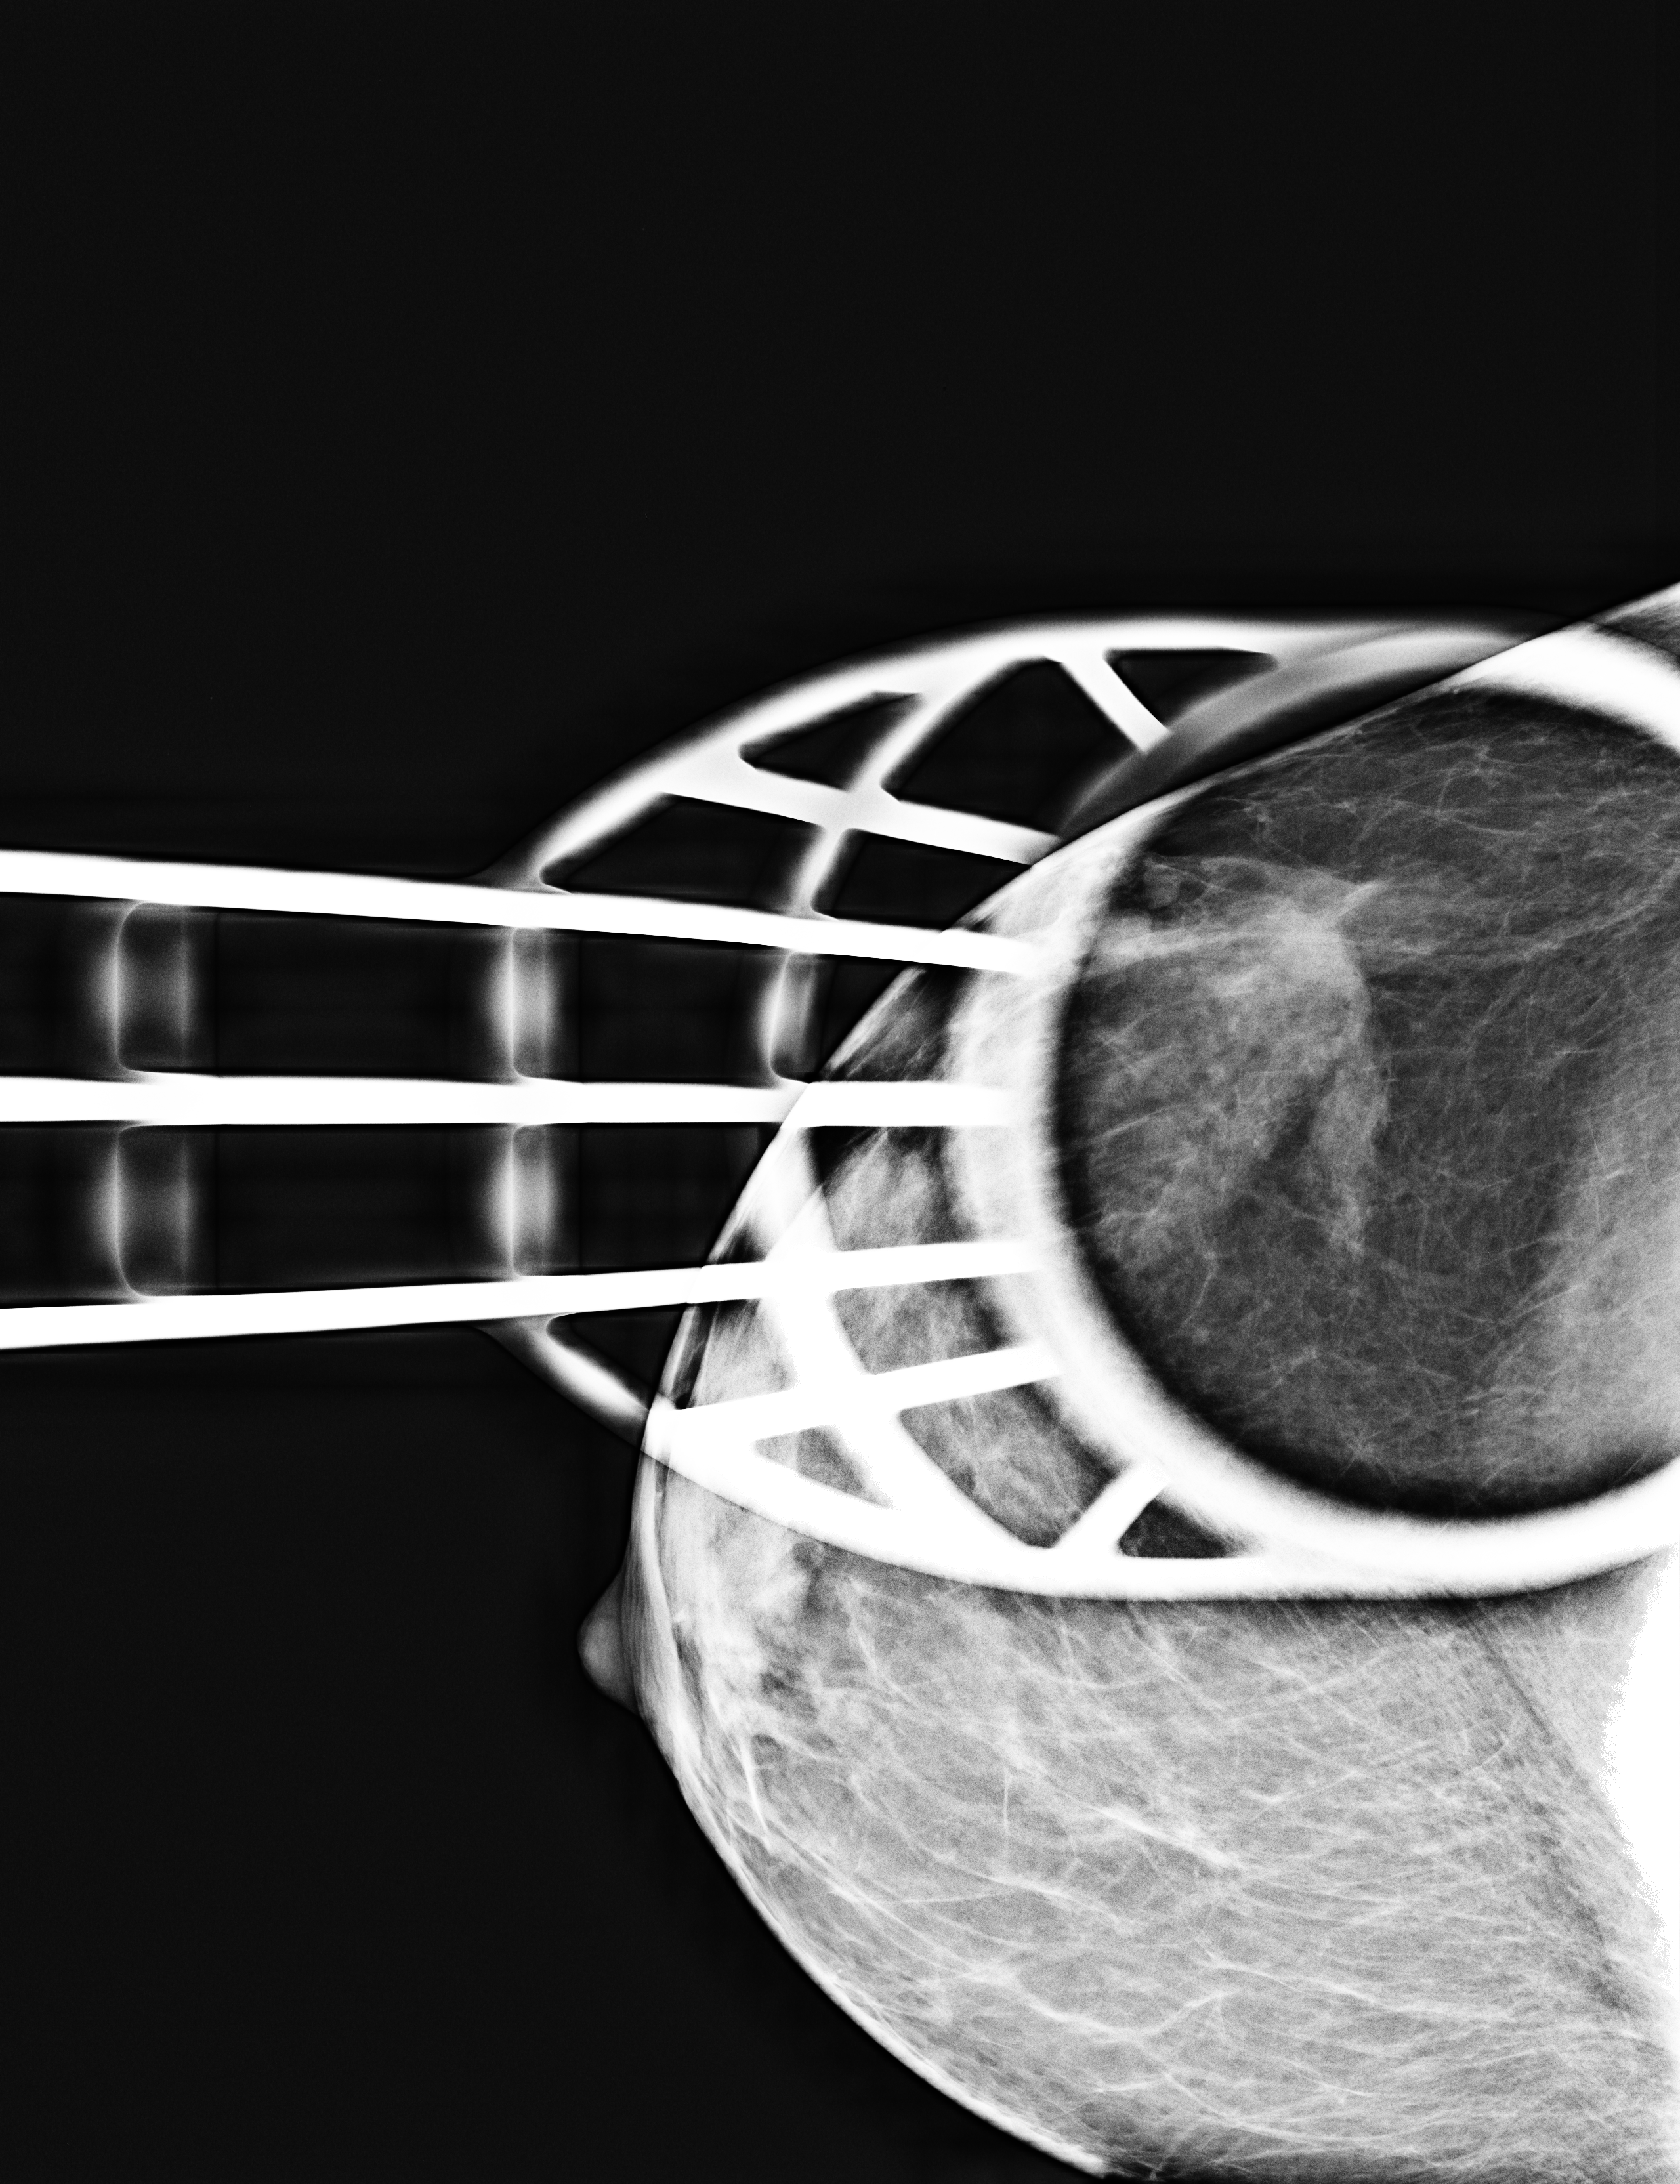
Additional (diagnostic) view; system: Selenia Dimensions.
Image type: full-field digital mammogram. Breast: right. Projection: craniocaudal (CC) view, spot compression.